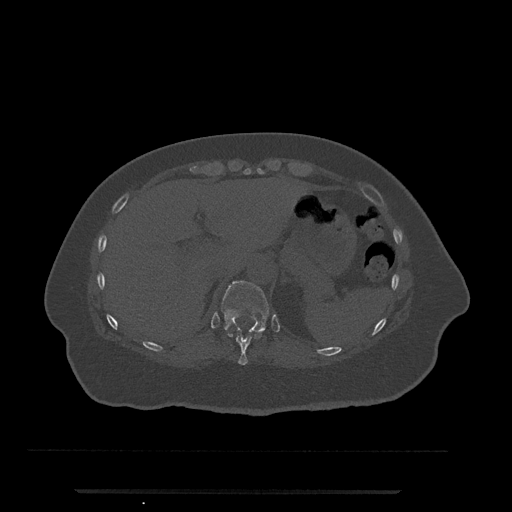
CT including the spine, one axial slice. Position 253 of 797 along the scan axis. Reconstruction kernel Br40s/3. 120 kVp. Bone window (W 1800 / L 400 HU). 0.5 mm slice thickness. 512 × 512 image matrix. Patient: female, 51 years. Case-level facts recorded for this patient, not image findings: primary cancer: neuro; vertebrae with lytic lesions (as recorded): T8.
Annotated regions visible in this slice (semi-automatically segmented with operator editing):
- T10 vertebra: bounding box [x1, y1, x2, y2] px = [227, 329, 265, 365]
- T11 vertebra: [221, 281, 269, 334]